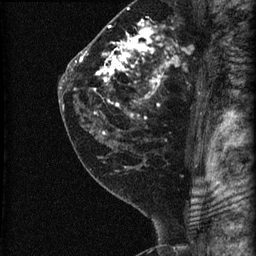
Breast MRI (dynamic contrast-enhanced), one sagittal slice. Slice 42 of 60 in the series (ordered by position). Dynamic contrast-enhanced series, image 2 of 3 at this slice position (ordered by acquisition). 1.5 T. TE 4.2 ms, TR 22.7 ms. 1.8 mm slice thickness. 256 × 256 image matrix, field of view 180 × 180 mm. Female patient, age 45 years. Case-level facts recorded for this patient, not image findings: setting: breast cancer imaged before/during neoadjuvant chemotherapy; receptor status: HR-positive, HER2-negative.
Structures marked on this image (semi-automatically segmented with operator editing):
- analysis volume of interest (the breast-tissue region the enhancement analysis was run in; not a lesion): bounding box <74,11,205,140> (left, top, right, bottom; pixels)
- tumour enhancement mask (voxels above the 90 % enhancement threshold inside the analysis volume of interest): <76,20,177,134>